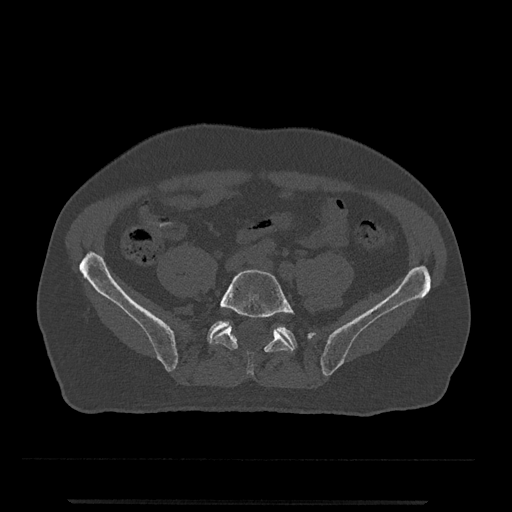
CT including the spine, one axial slice. Slice 61 of 797 in the series (ordered by position). Bone window (W 1800 / L 400 HU). 512 × 512 image matrix, field of view 419 × 419 mm. Patient: male, 63 years. Case-level facts recorded for this patient, not image findings: primary cancer: prostate.
Structures marked on this image (semi-automatic segmentation, software-assisted and operator-edited):
- L5 vertebra: bounding box <211,269,295,375> (left, top, right, bottom; pixels)